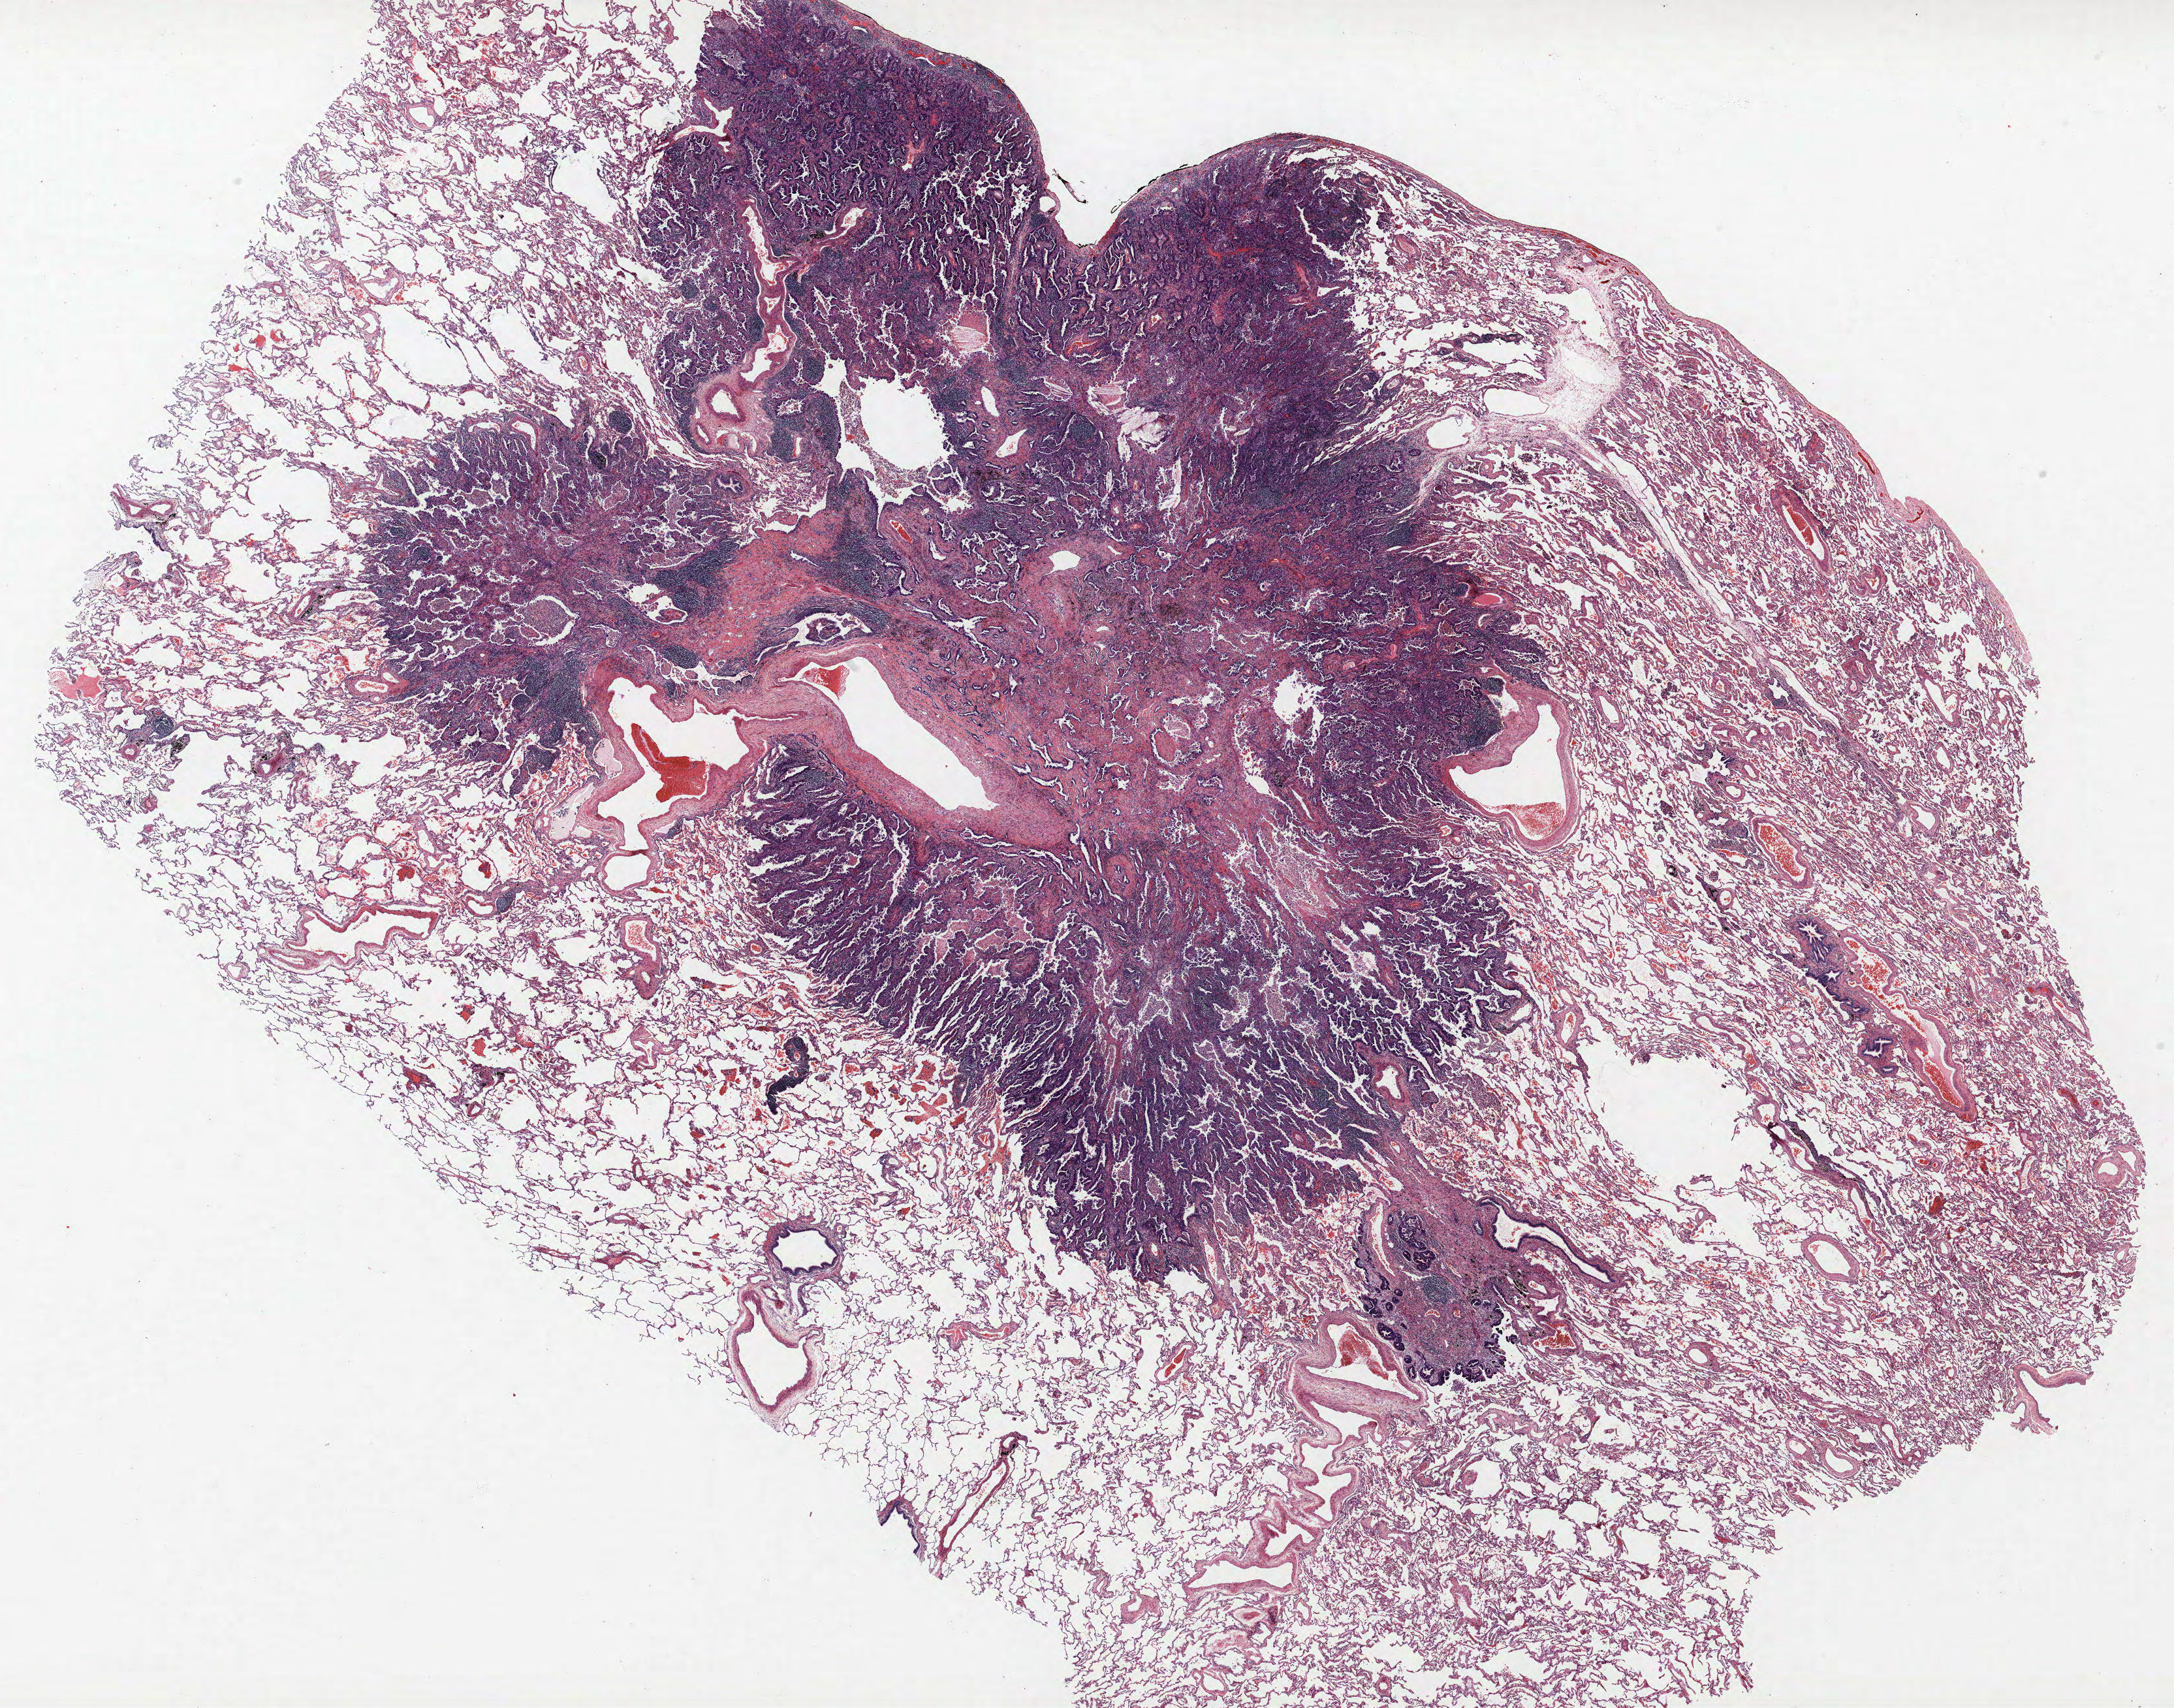
Whole-slide histology image, H&E-stained — a low-resolution overview of the entire scanned area, about 26.6 x 20.9 mm (acquisition: 40x scan). FFPE section. Lung tissue. Female patient, aged 59 at enrolment. Grade: poorly differentiated (G3).
- tumour size (pathology): 22 mm
- participant's lung-cancer diagnosis: Adenocarcinoma, NOS (ICD-O-3 8140/3)
- stage (AJCC 6th edition): IA
- primary tumour location (clinical record): left lower lobe